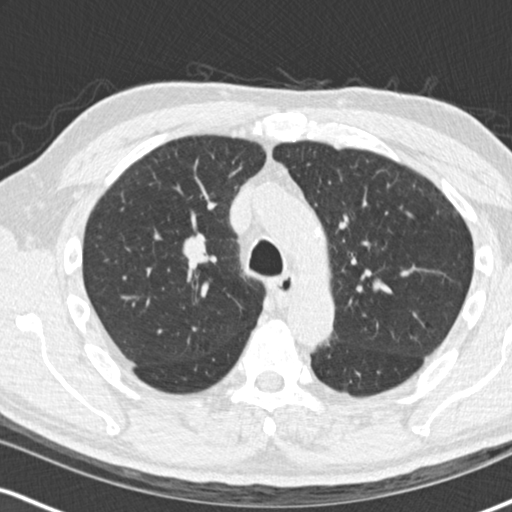
Low-dose screening chest CT, one axial slice. Position 109 of 170 along the scan axis. 120 kVp. Lung window (W 1500 / L -600 HU). 512 × 512 image matrix.
Structures marked on this image (manually delineated by an expert):
- lesion 1 (tumor, upper lobe of right lung): bounding box [x1, y1, x2, y2] px = [183, 232, 209, 264]